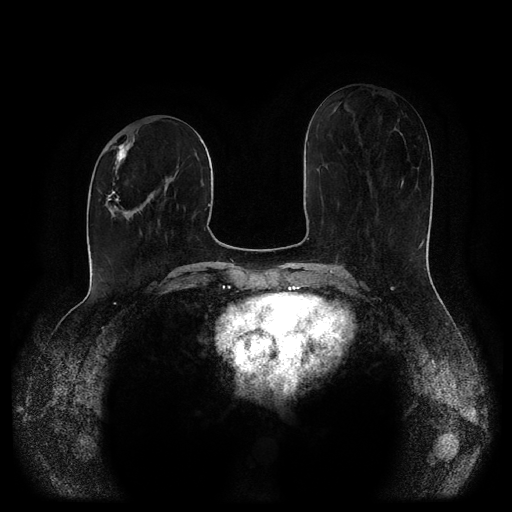
Breast MRI (dynamic contrast-enhanced, multi-phase), one axial slice; position 40 of 116 along the scan axis; dynamic contrast-enhanced series, time point 2 of 5 at this slice position (early post-contrast); 1.5 T; TE 2.6 ms, TR 5.2 ms; 2 mm slice thickness; 512 × 512 image matrix, field of view 380 × 380 mm. Patient: female, 52 years.
Annotated regions visible in this slice (semi-automatically segmented with operator editing):
- breast lesion (labelled 'tumour' in the annotation; benign lesions carry a separate 'benign' label): box from (x=98, y=138) to (x=135, y=219) px